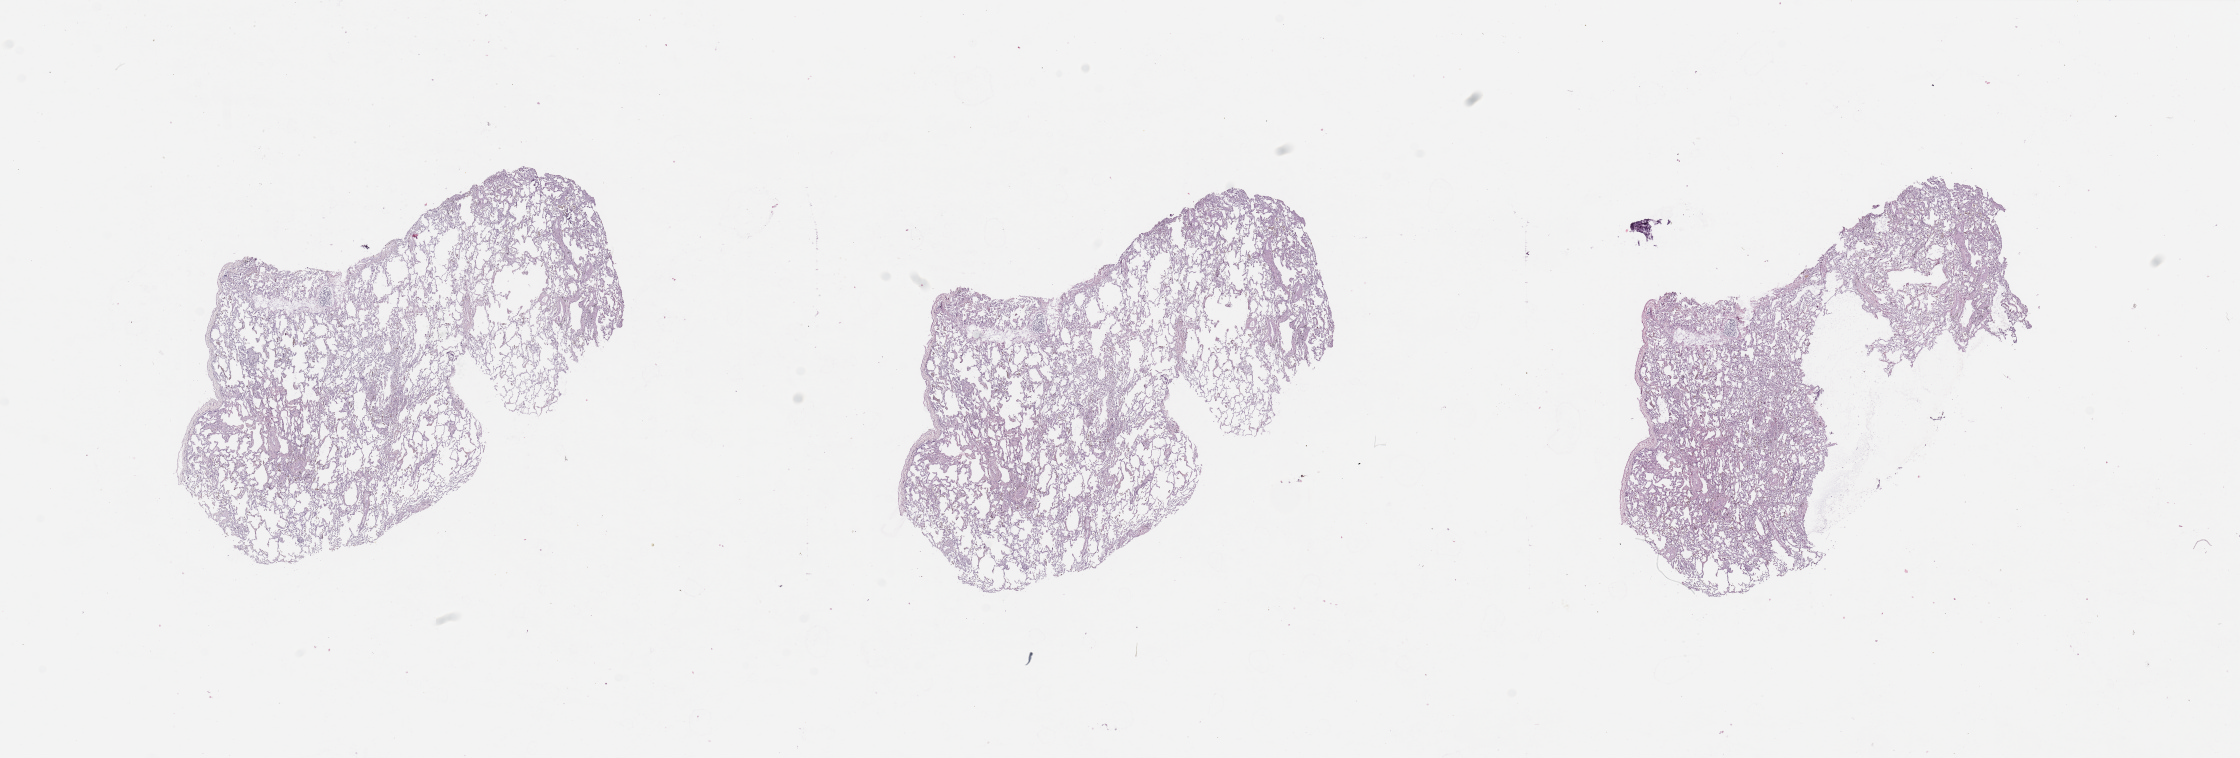
Whole-slide histology image, H&E-stained — shown as a low-resolution overview of the whole scanned area (about 35.4 x 12.0 mm, from a 20x scan); normal (non-tumour) tissue sample, sampled site: lung. Patient: male, age 51 years.
This section: normal (non-tumour) tissue from the same patient. Patient diagnosis: Adenocarcinoma, NOS.